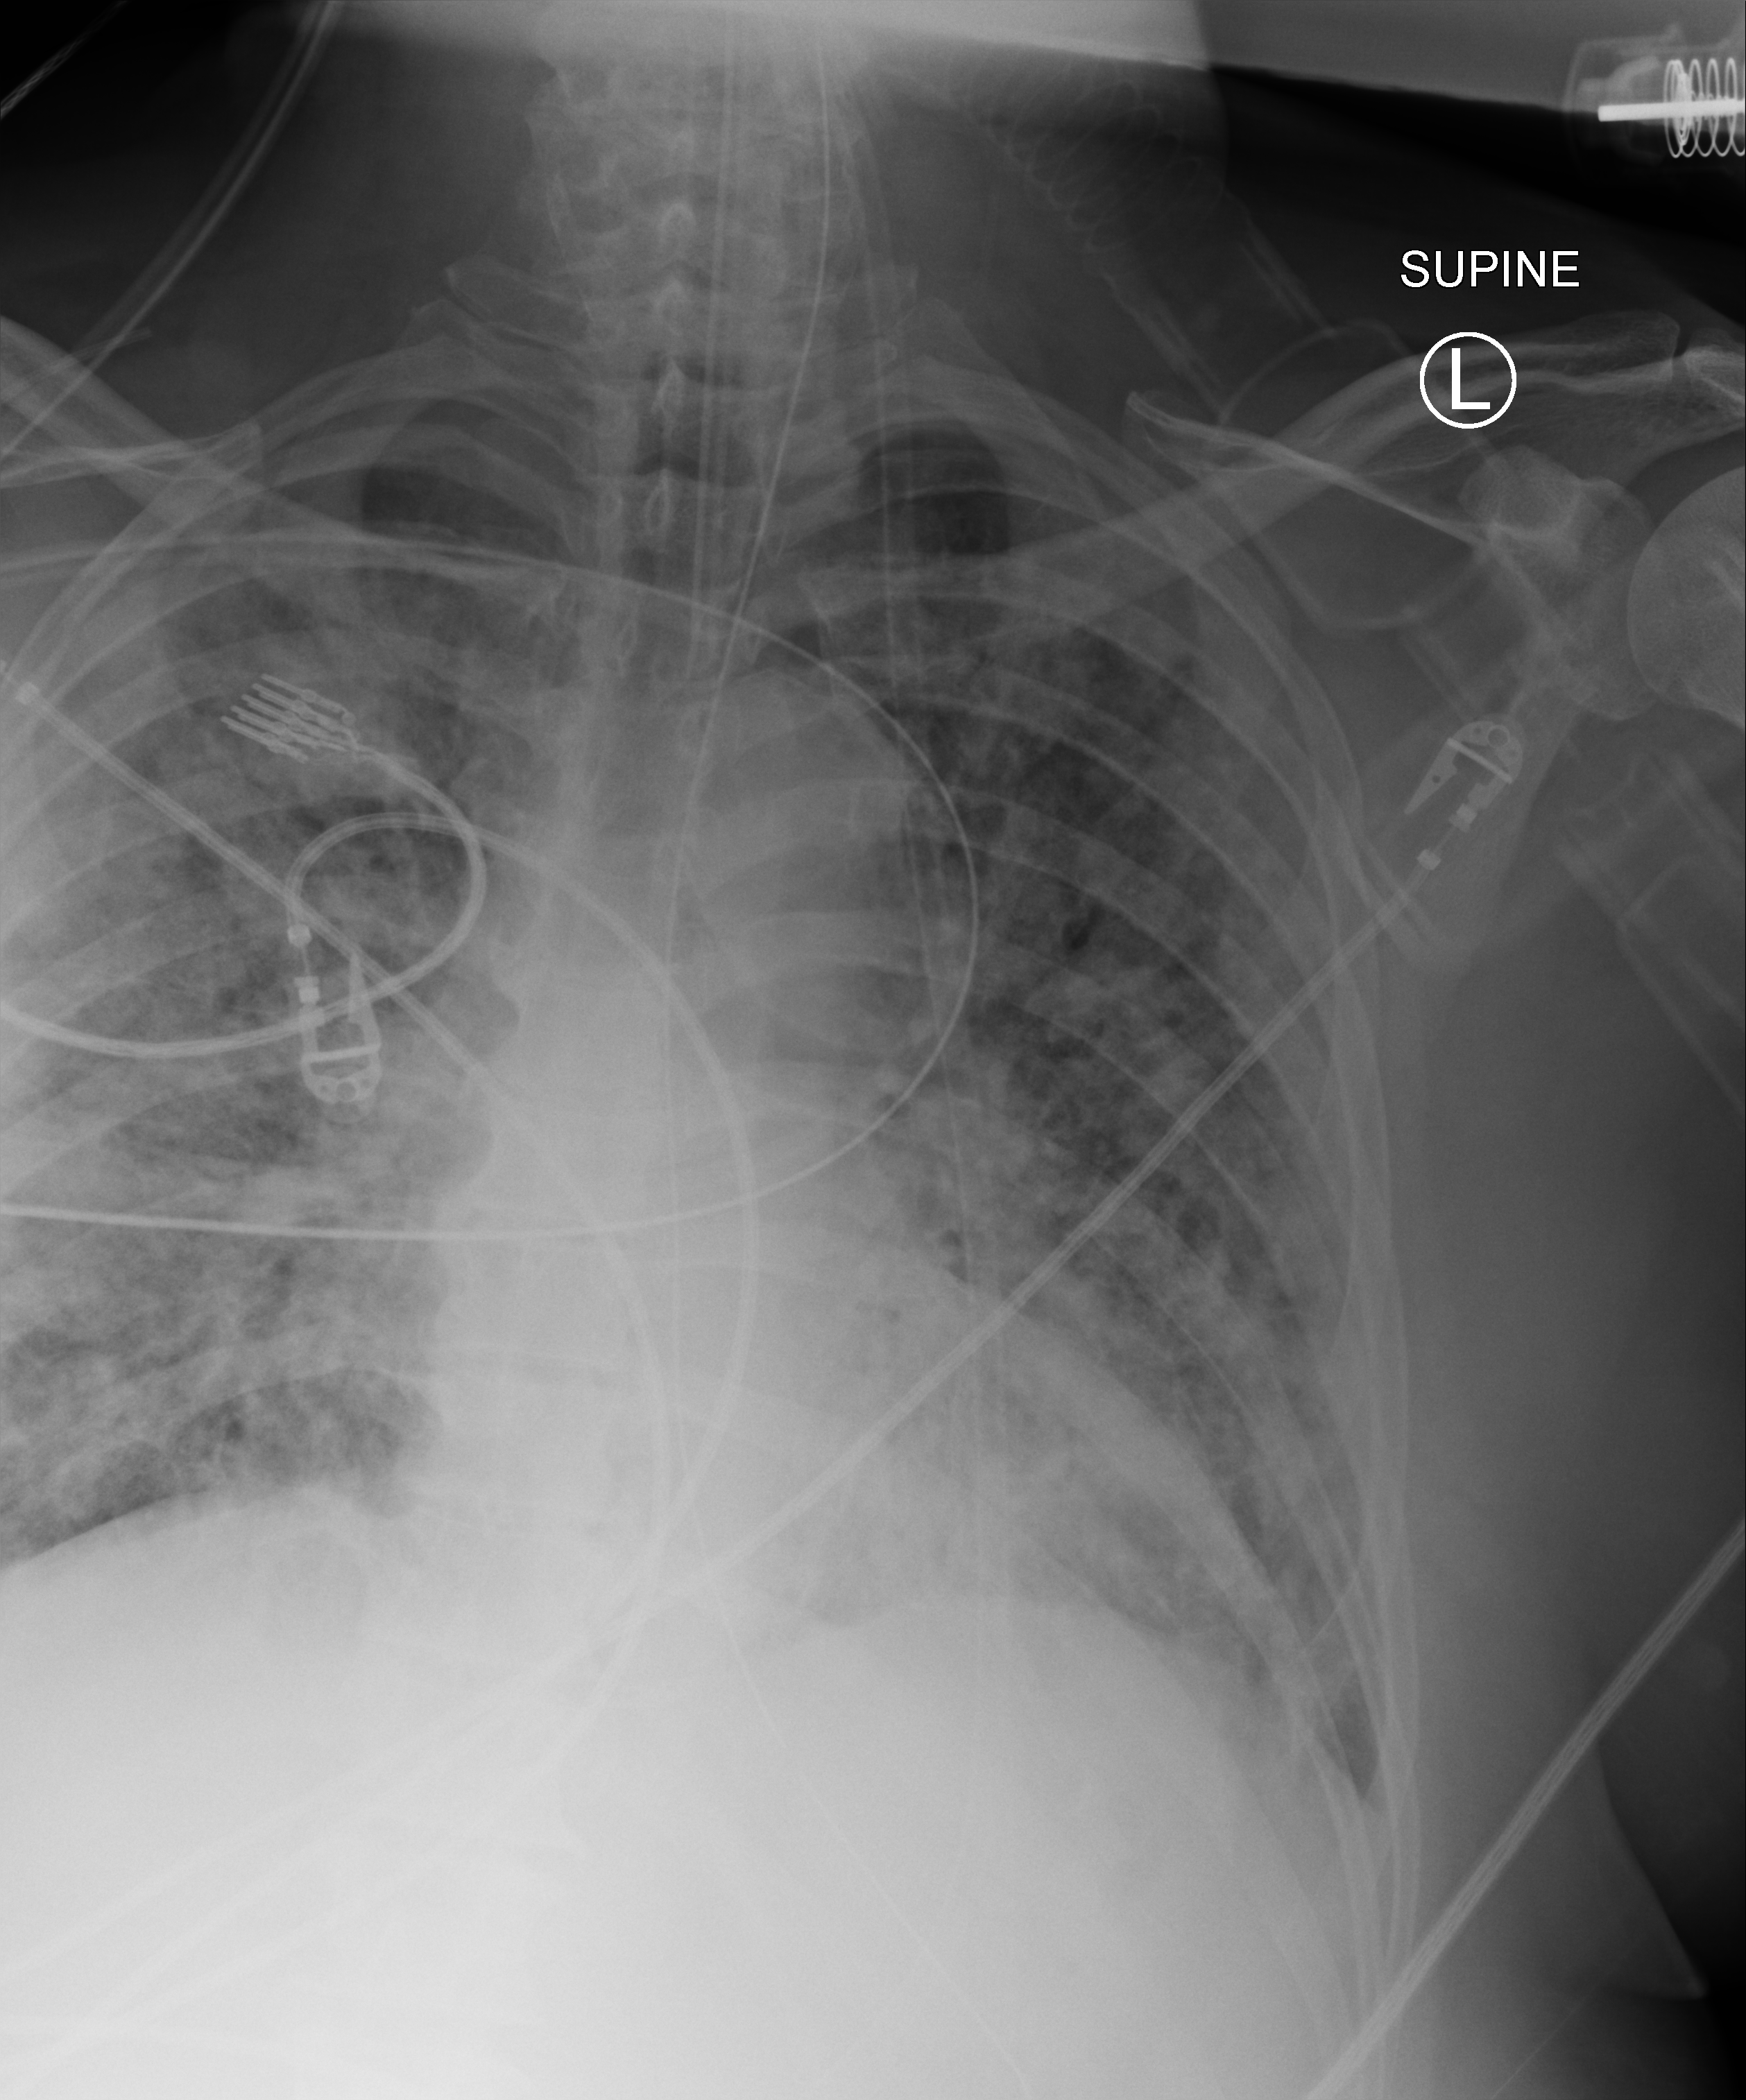
Chest X-ray (portable); anteroposterior (AP) projection. Patient hospitalised with COVID-19; male, aged 60–74 years.
Hospital-stay facts (about this admission, not read from this image; timing relative to this image not recorded):
- smoking status (admission record): former
- mechanically ventilated during this hospital stay: yes